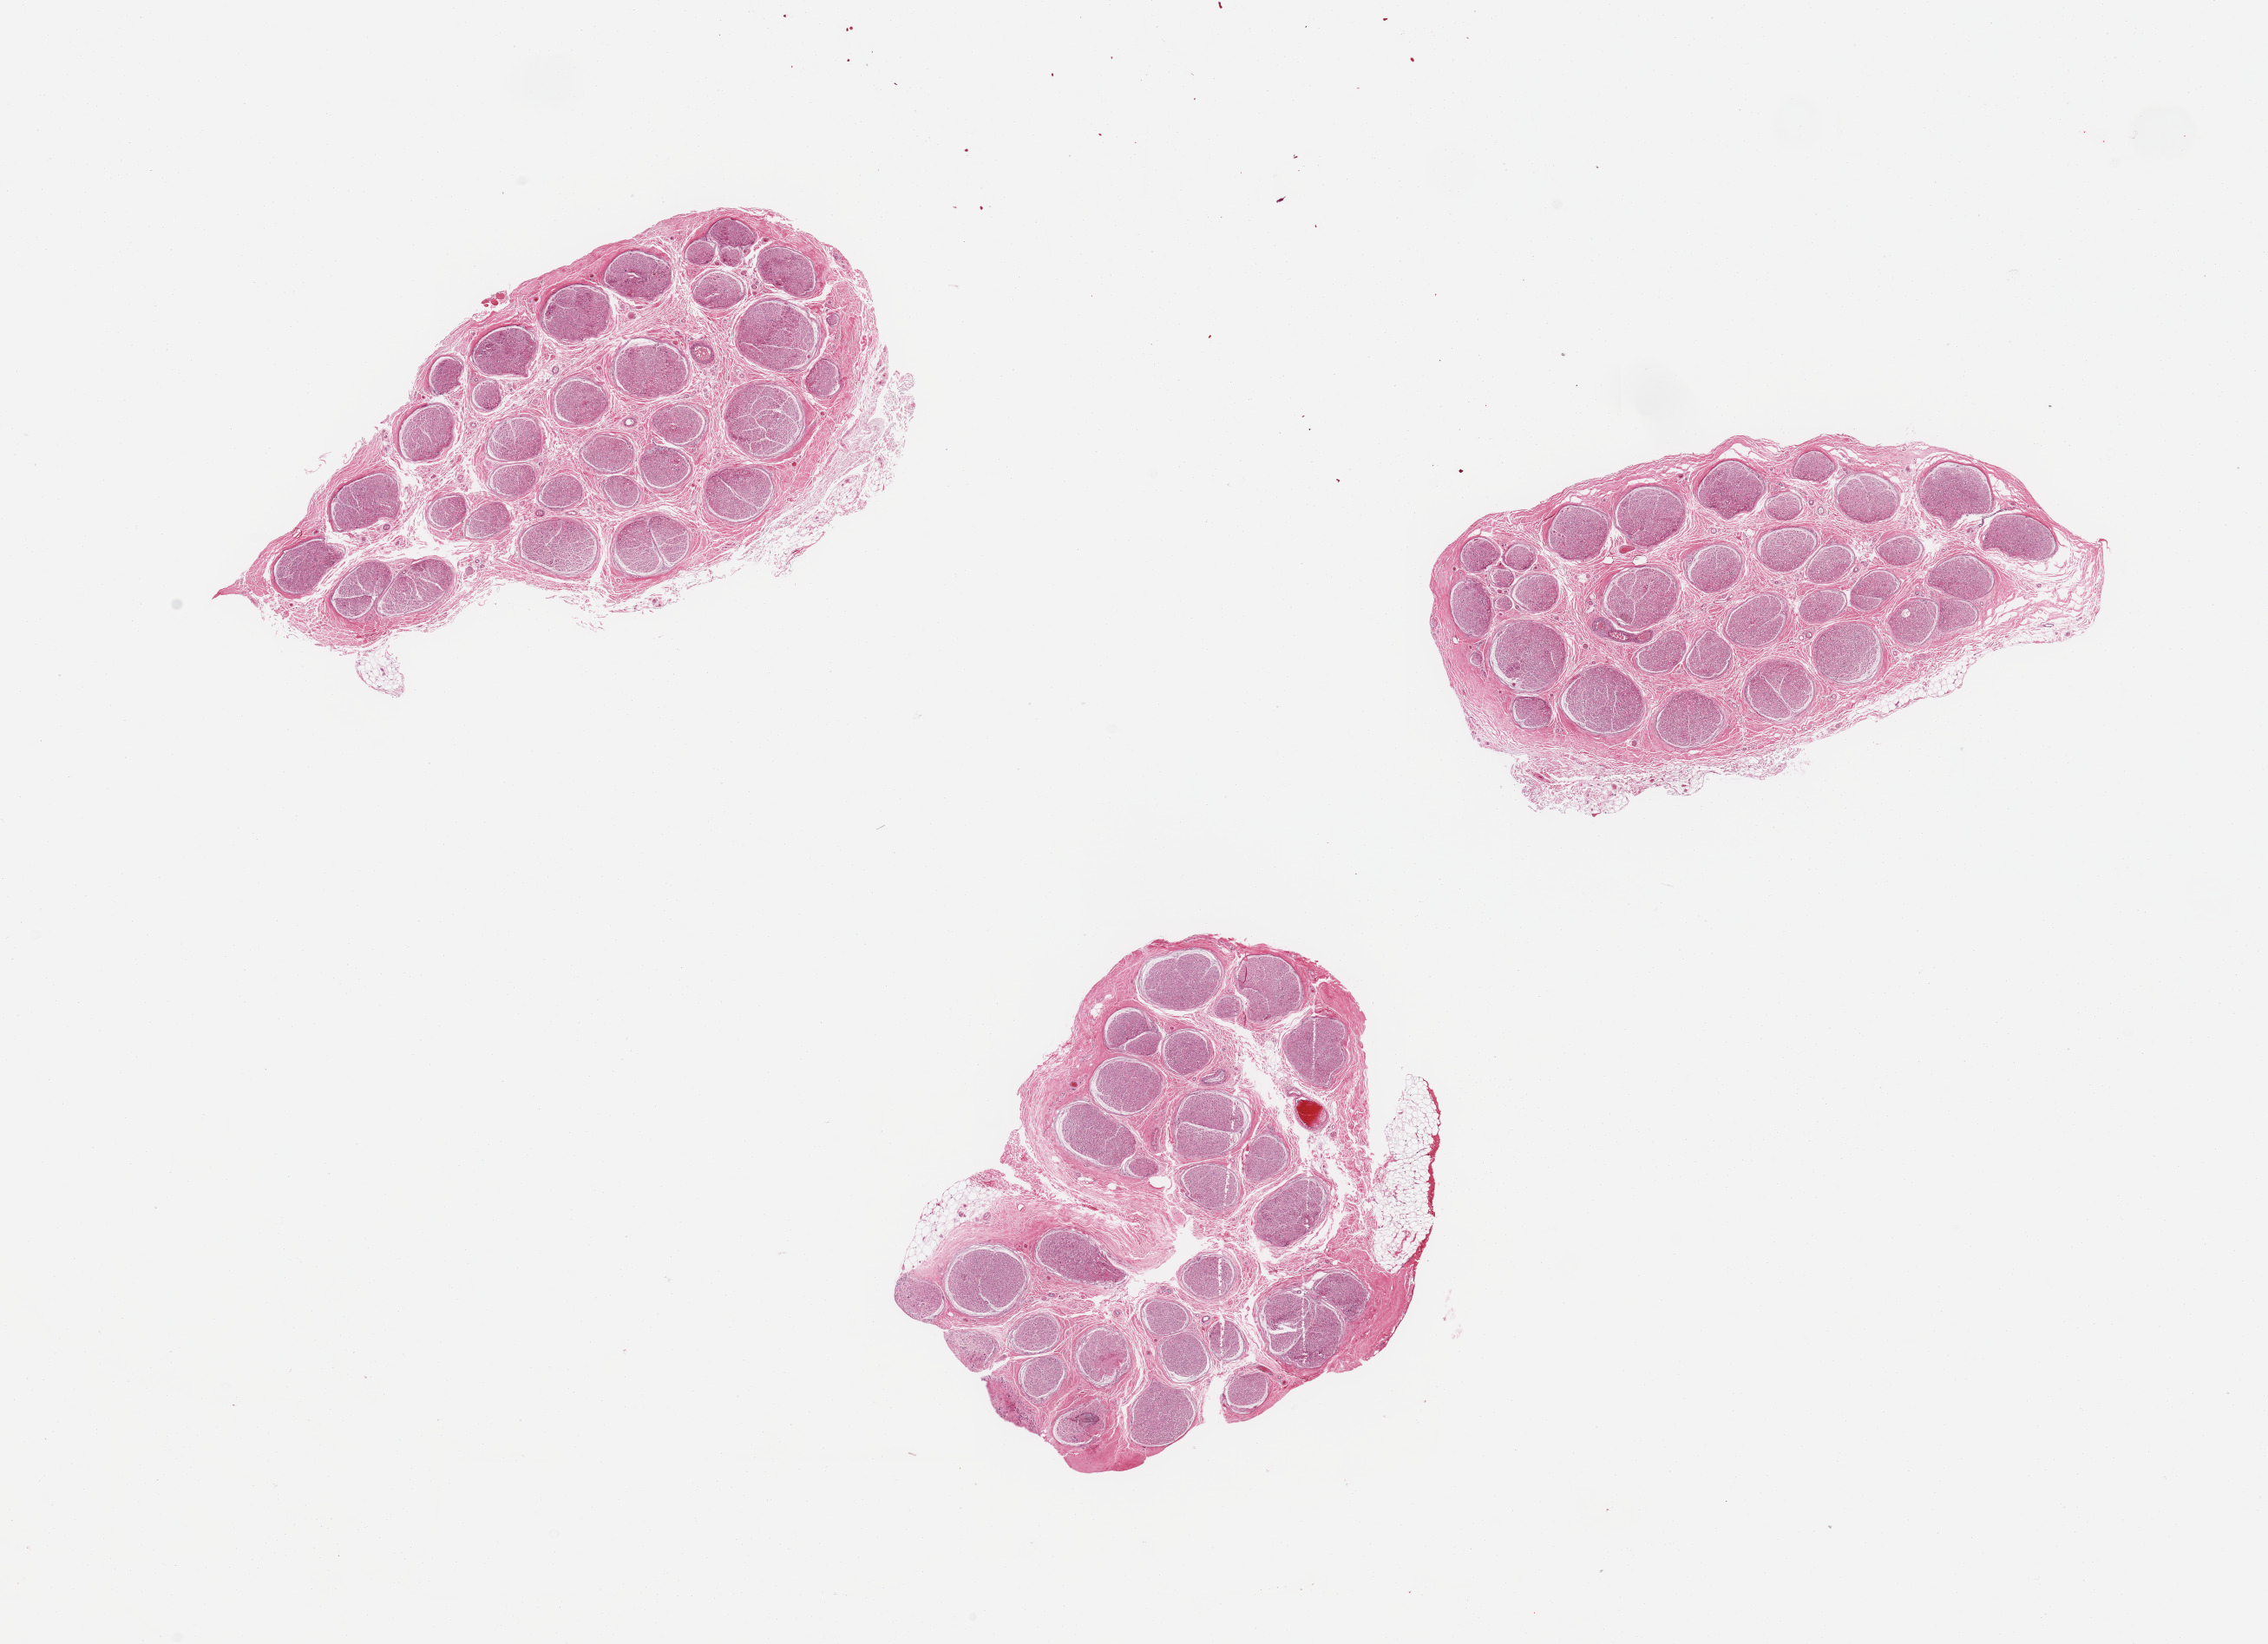
H&E whole-slide image, brightfield — shown as a low-resolution overview of the whole scanned area (about 20.7 x 15.0 mm, acquisition: 20x scan). PAXgene-fixed, paraffin-embedded tissue. Sampled site (target tissue): tibial nerve. Donor tissue sample.
Reviewer comment on this tissue sample: 3 pieces; 10% external fat.